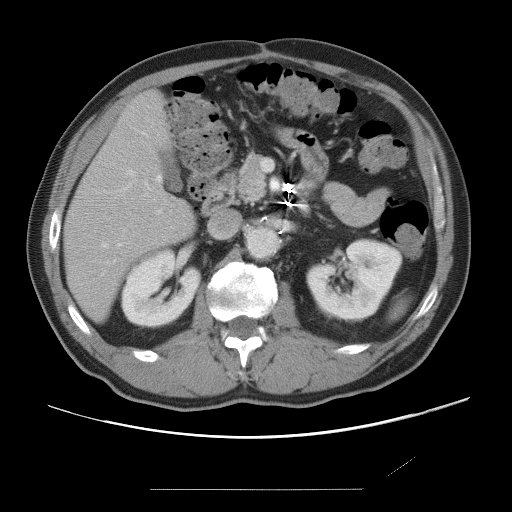
Contrast-enhanced abdominal CT, one axial slice; position 33 of 87 along the scan axis; intravenous contrast given; soft-tissue window (W 400 / L 40 HU); 5 mm slice thickness; 512 × 512 image matrix, field of view 406 × 406 mm. Male patient, age 74 years. From the clinical record (not read from this slice): diagnosis: colorectal cancer liver metastases, imaged before liver resection; multiple liver metastases: yes; largest metastasis: 1.1 cm; disease in both lobes: no.
Annotated regions visible in this slice (expert manual segmentation):
- hepatic veins: box from (x=102, y=132) to (x=161, y=247) px
- liver: (x=66, y=94)–(x=195, y=319)
- planned liver remnant (the part of the liver to remain after resection): (x=66, y=93)–(x=195, y=319)
- portal vein (with intrahepatic branches): (x=147, y=185)–(x=162, y=213)